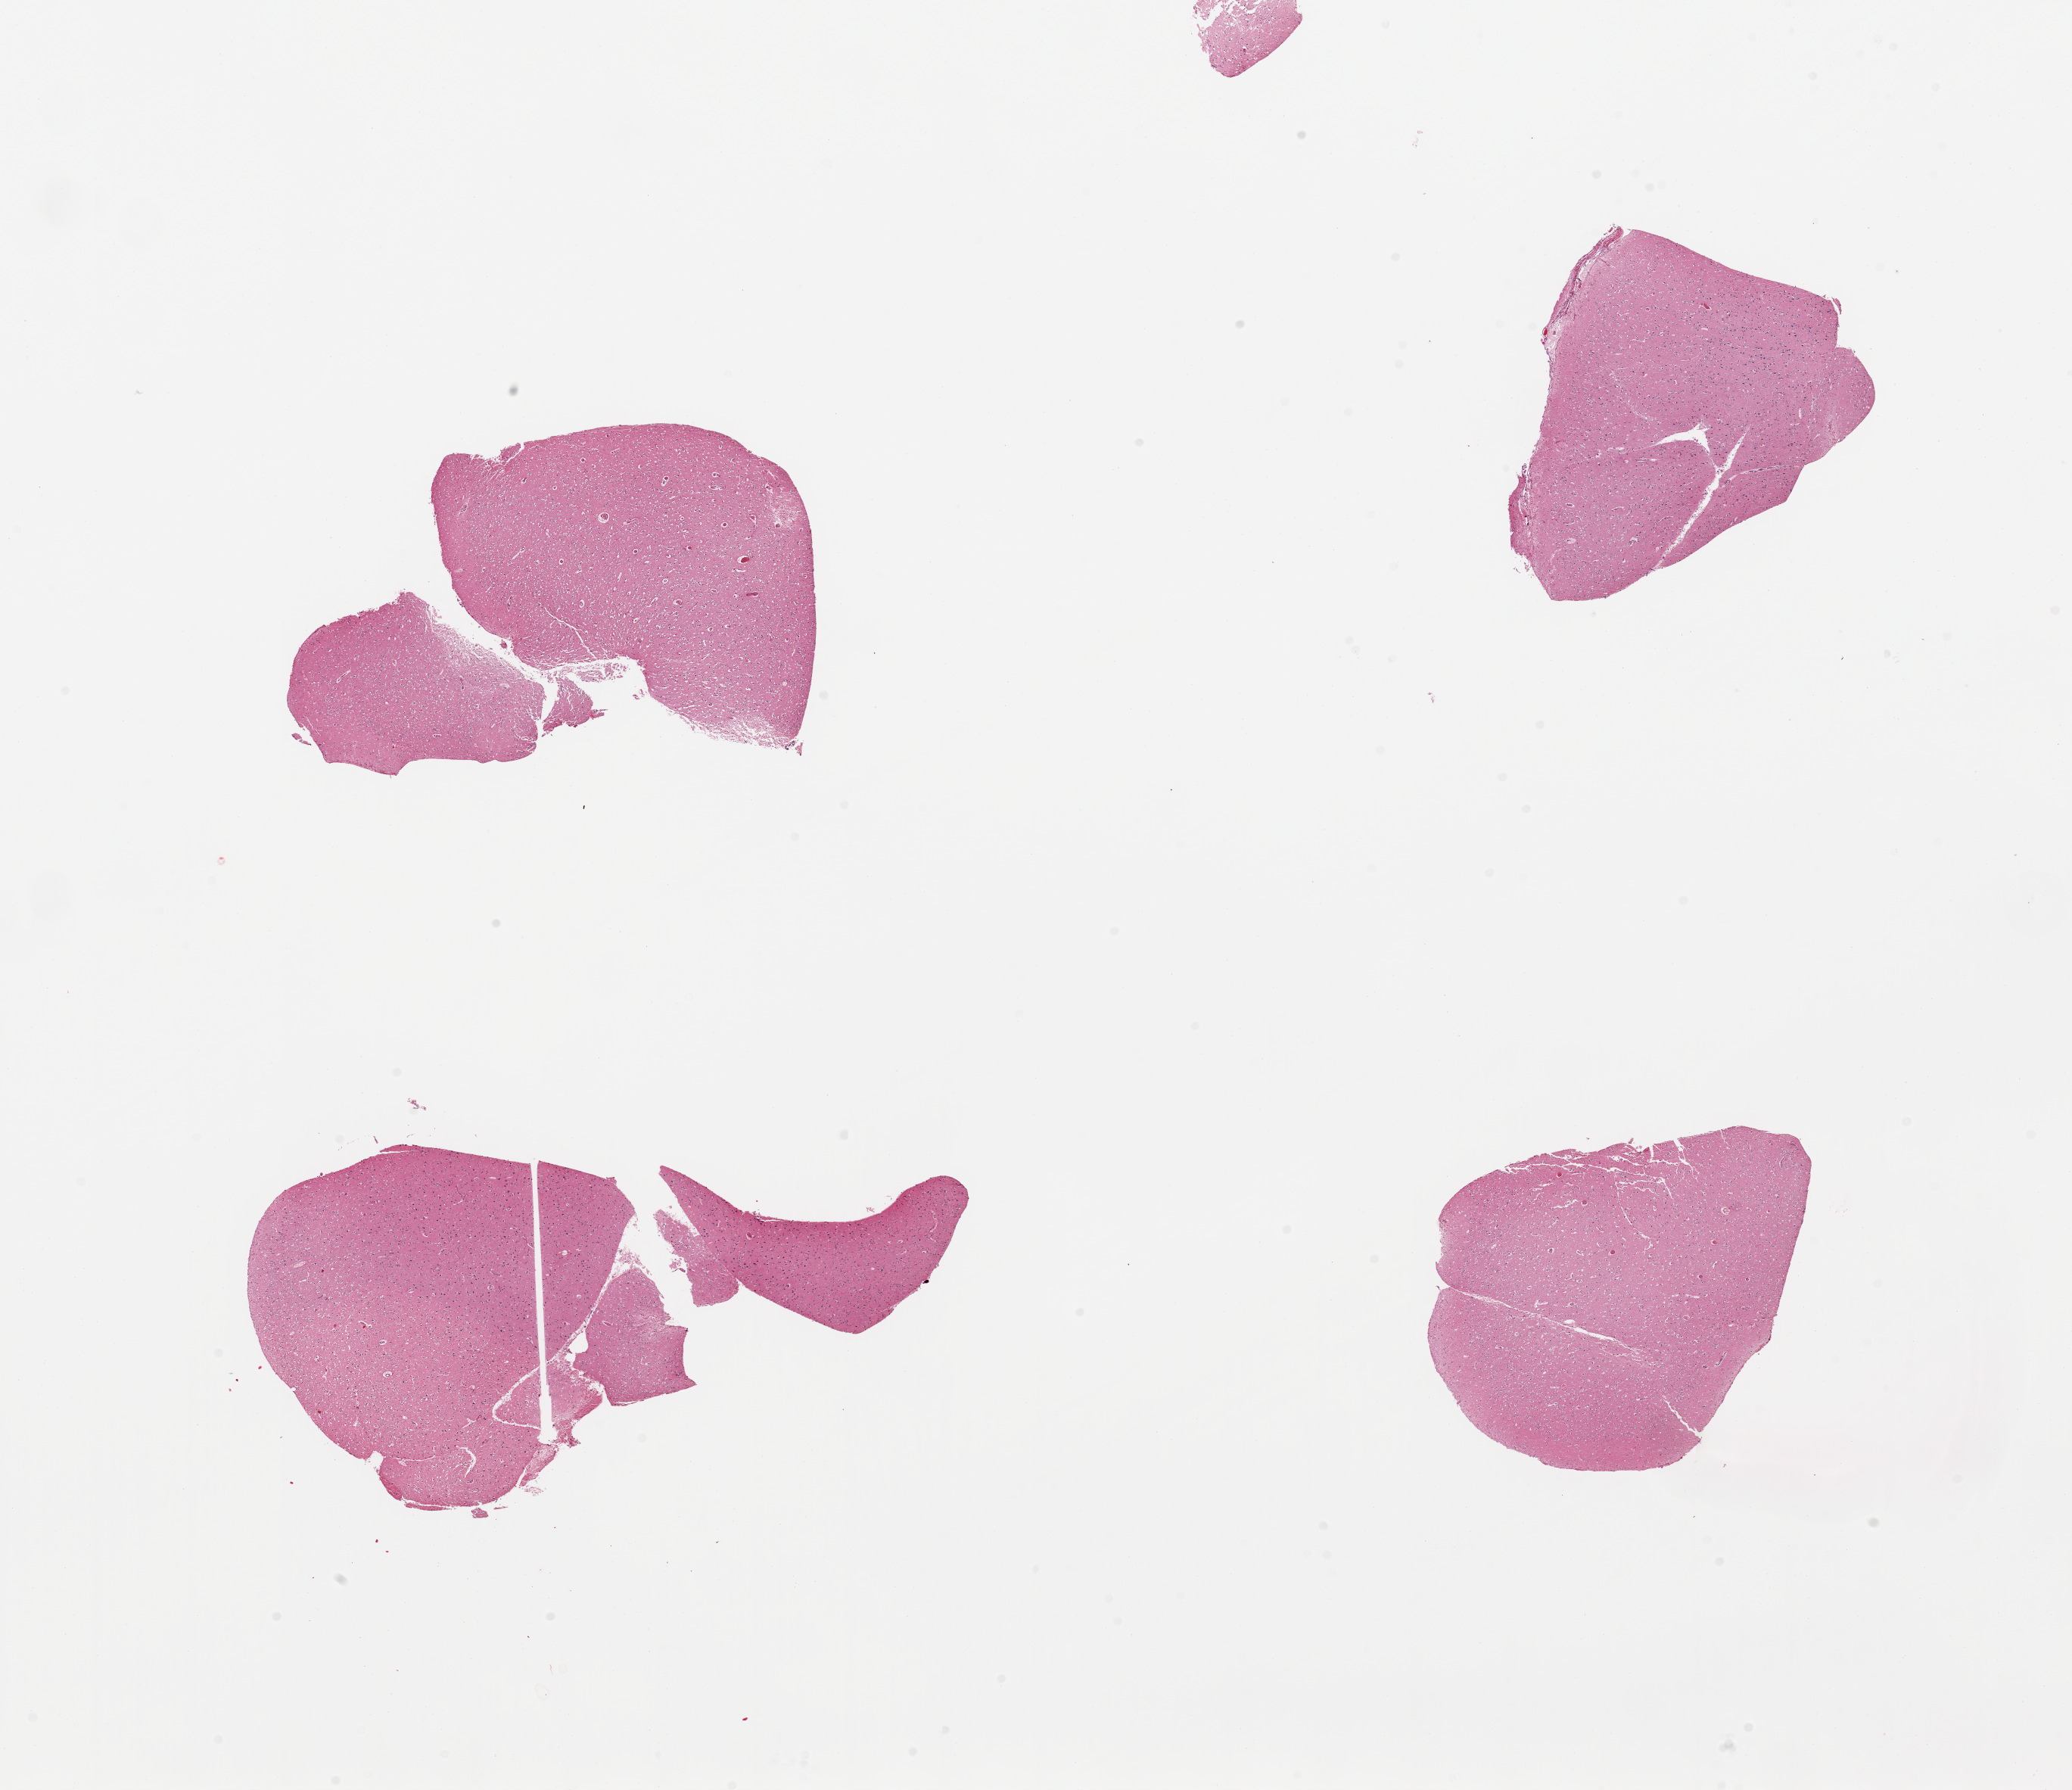
Whole-slide image, hematoxylin and eosin (H&E) stain — low-resolution overview of the scanned area, about 21.7 x 18.7 mm (from a 20x scan).
Specimen: PAXgene-fixed paraffin-embedded (PFPE) section; sampled site (target tissue): cerebellum; donor tissue sample.